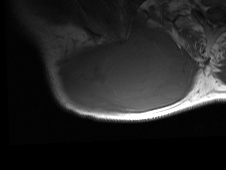
MRI of an extremity soft-tissue mass, one axial slice; position 48 of 81 along the scan axis; MR volume resampled by the dataset authors to the PET/CT grid (not the native acquisition matrix); 3.27 mm slice thickness; 226 × 170 image matrix, field of view 221 × 166 mm. Male patient. Case-level facts recorded for this patient, not image findings: histological type: pleiomorphic spindle cell undifferentiated; grade: high; site of the primary tumour: right parascapusular.
Annotated regions visible in this slice (expert contour drawn on MRI and transferred to this co-registered scan by the dataset authors):
- gross tumour volume including surrounding oedema: bounding box <53,24,196,116> (left, top, right, bottom; pixels)
- gross tumour volume (mass): <57,29,187,112>